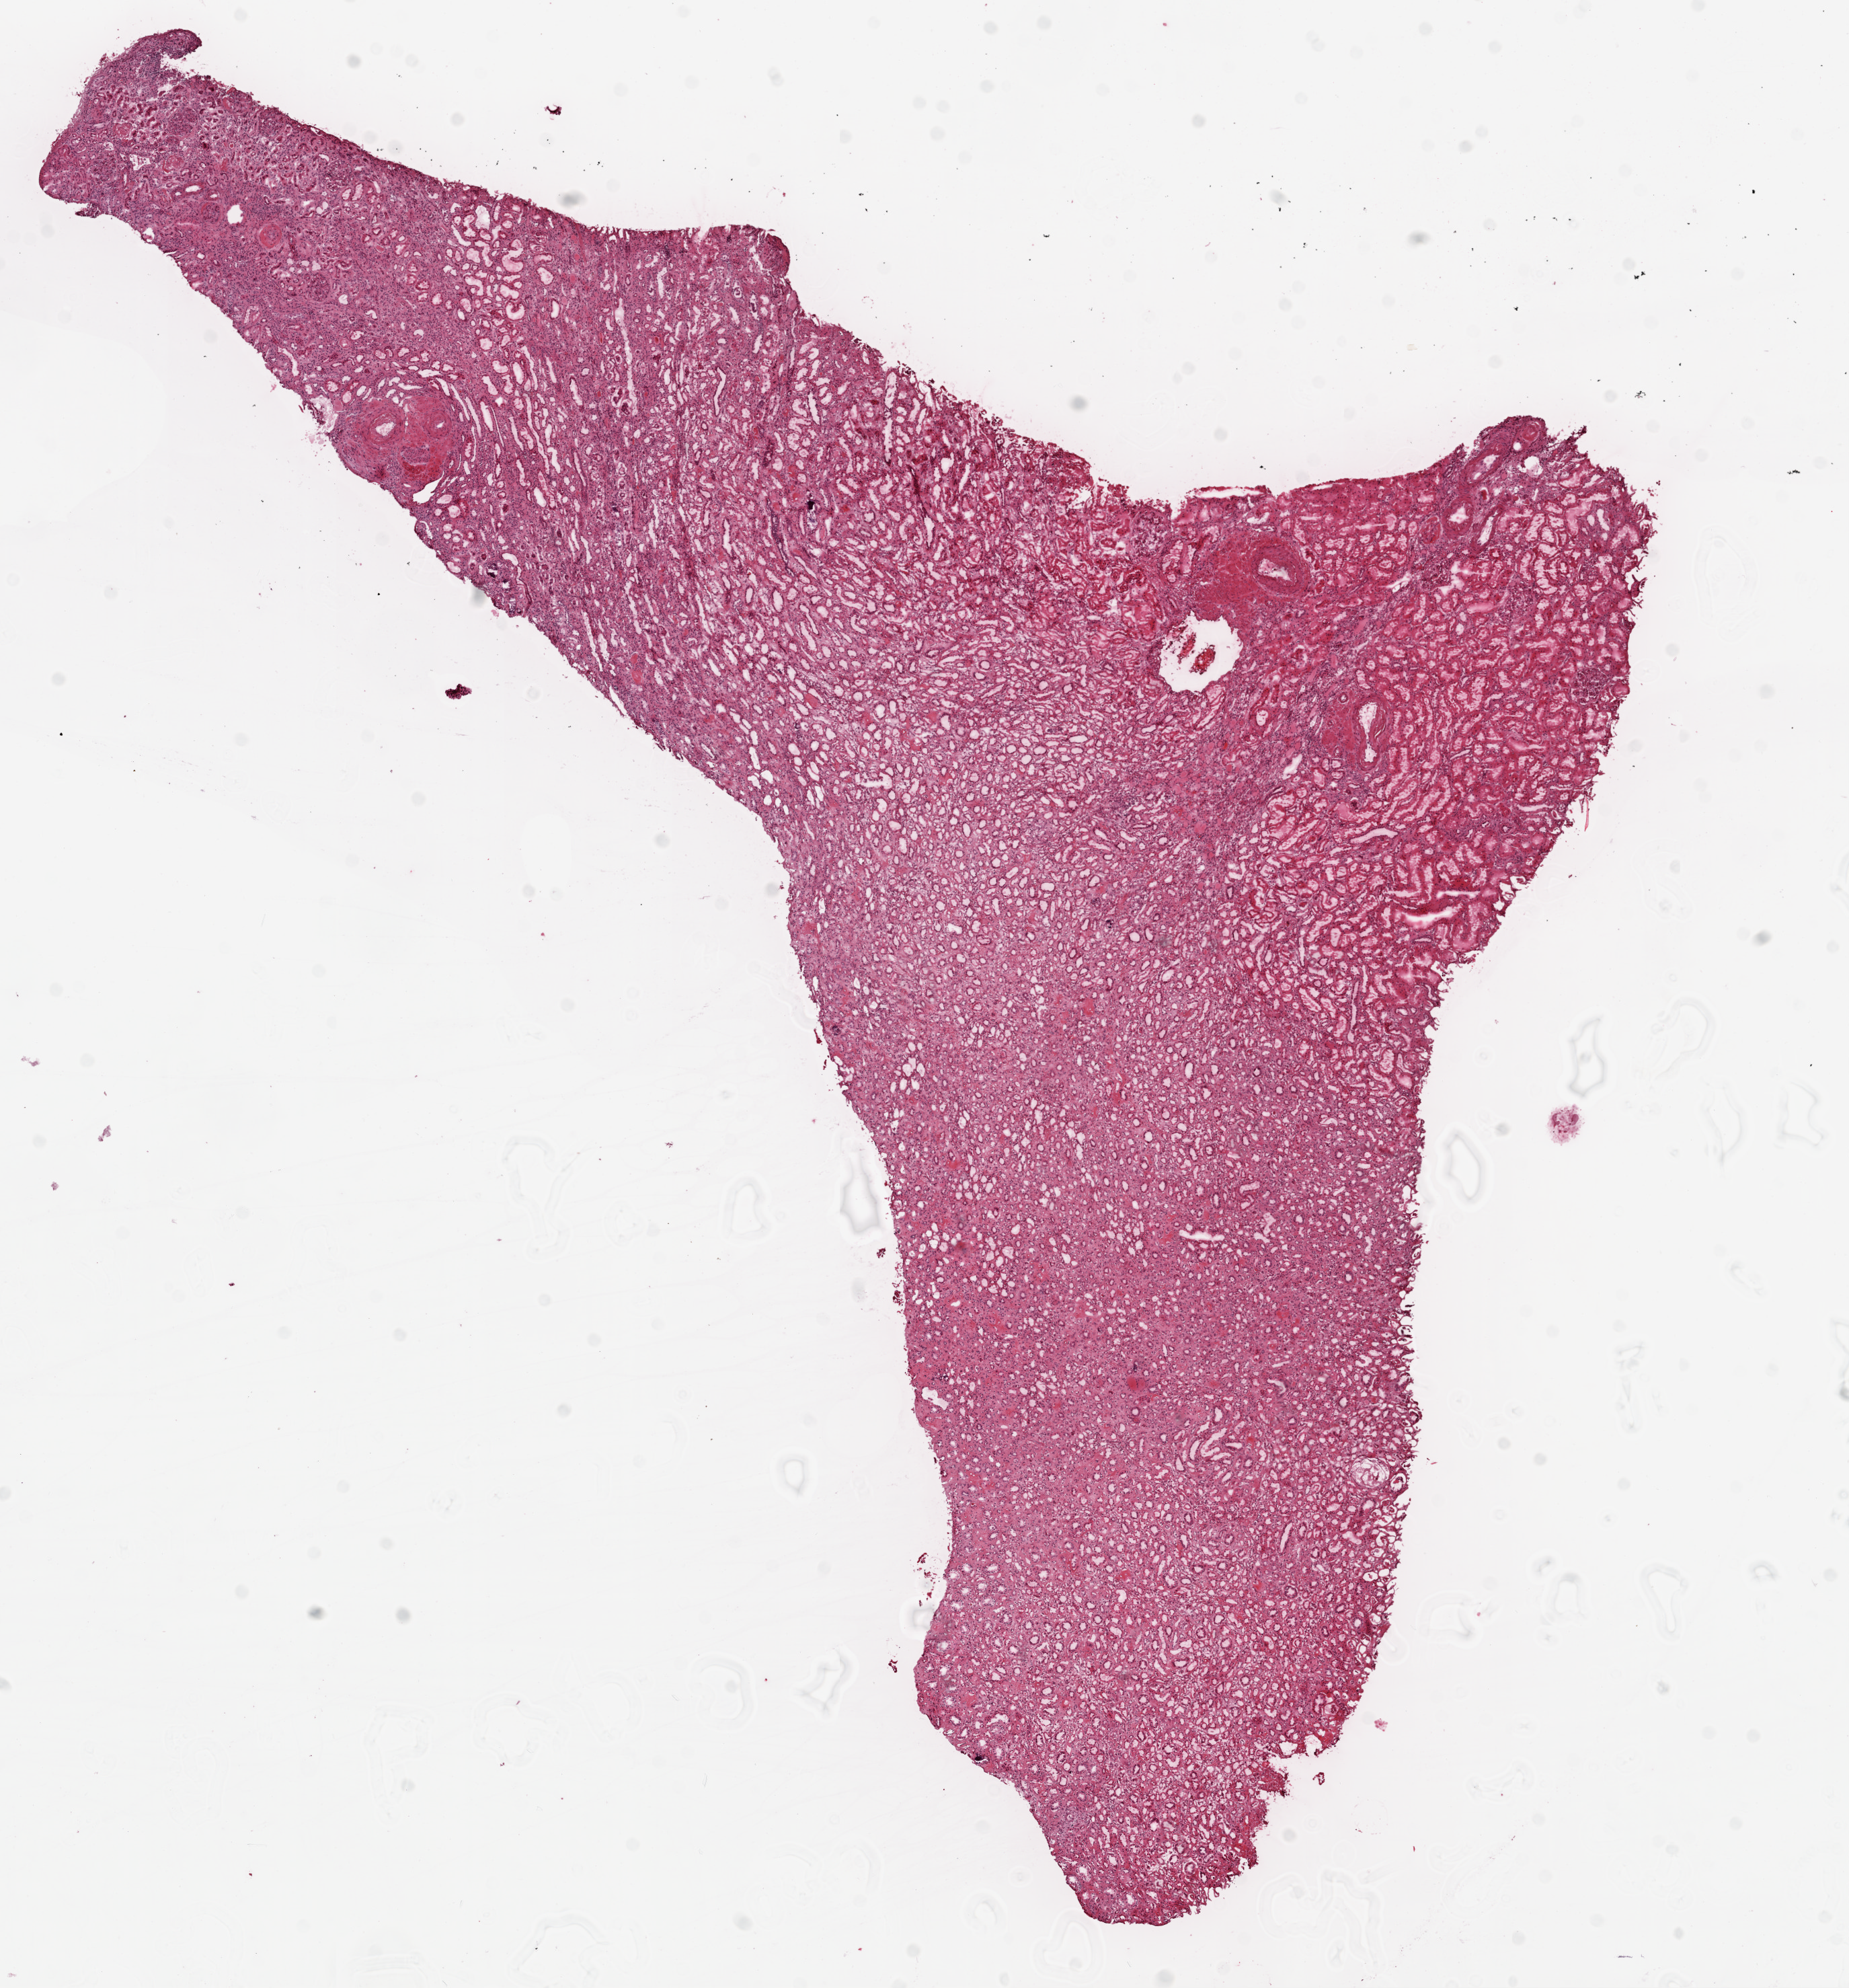
Digitized Hematoxylin and eosin (H&E) stained tissue section (whole slide), a low-resolution overview of the entire scanned area, about 11.0 x 11.9 mm (slide scanned at 20x); frozen section from the top of the tissue portion; kidney, solid tissue normal (non-tumour tissue) sample. Male, age 57 years at initial diagnosis.
This section: solid tissue normal (non-tumour) sample from the same patient. Patient diagnosis: Clear cell adenocarcinoma, NOS.